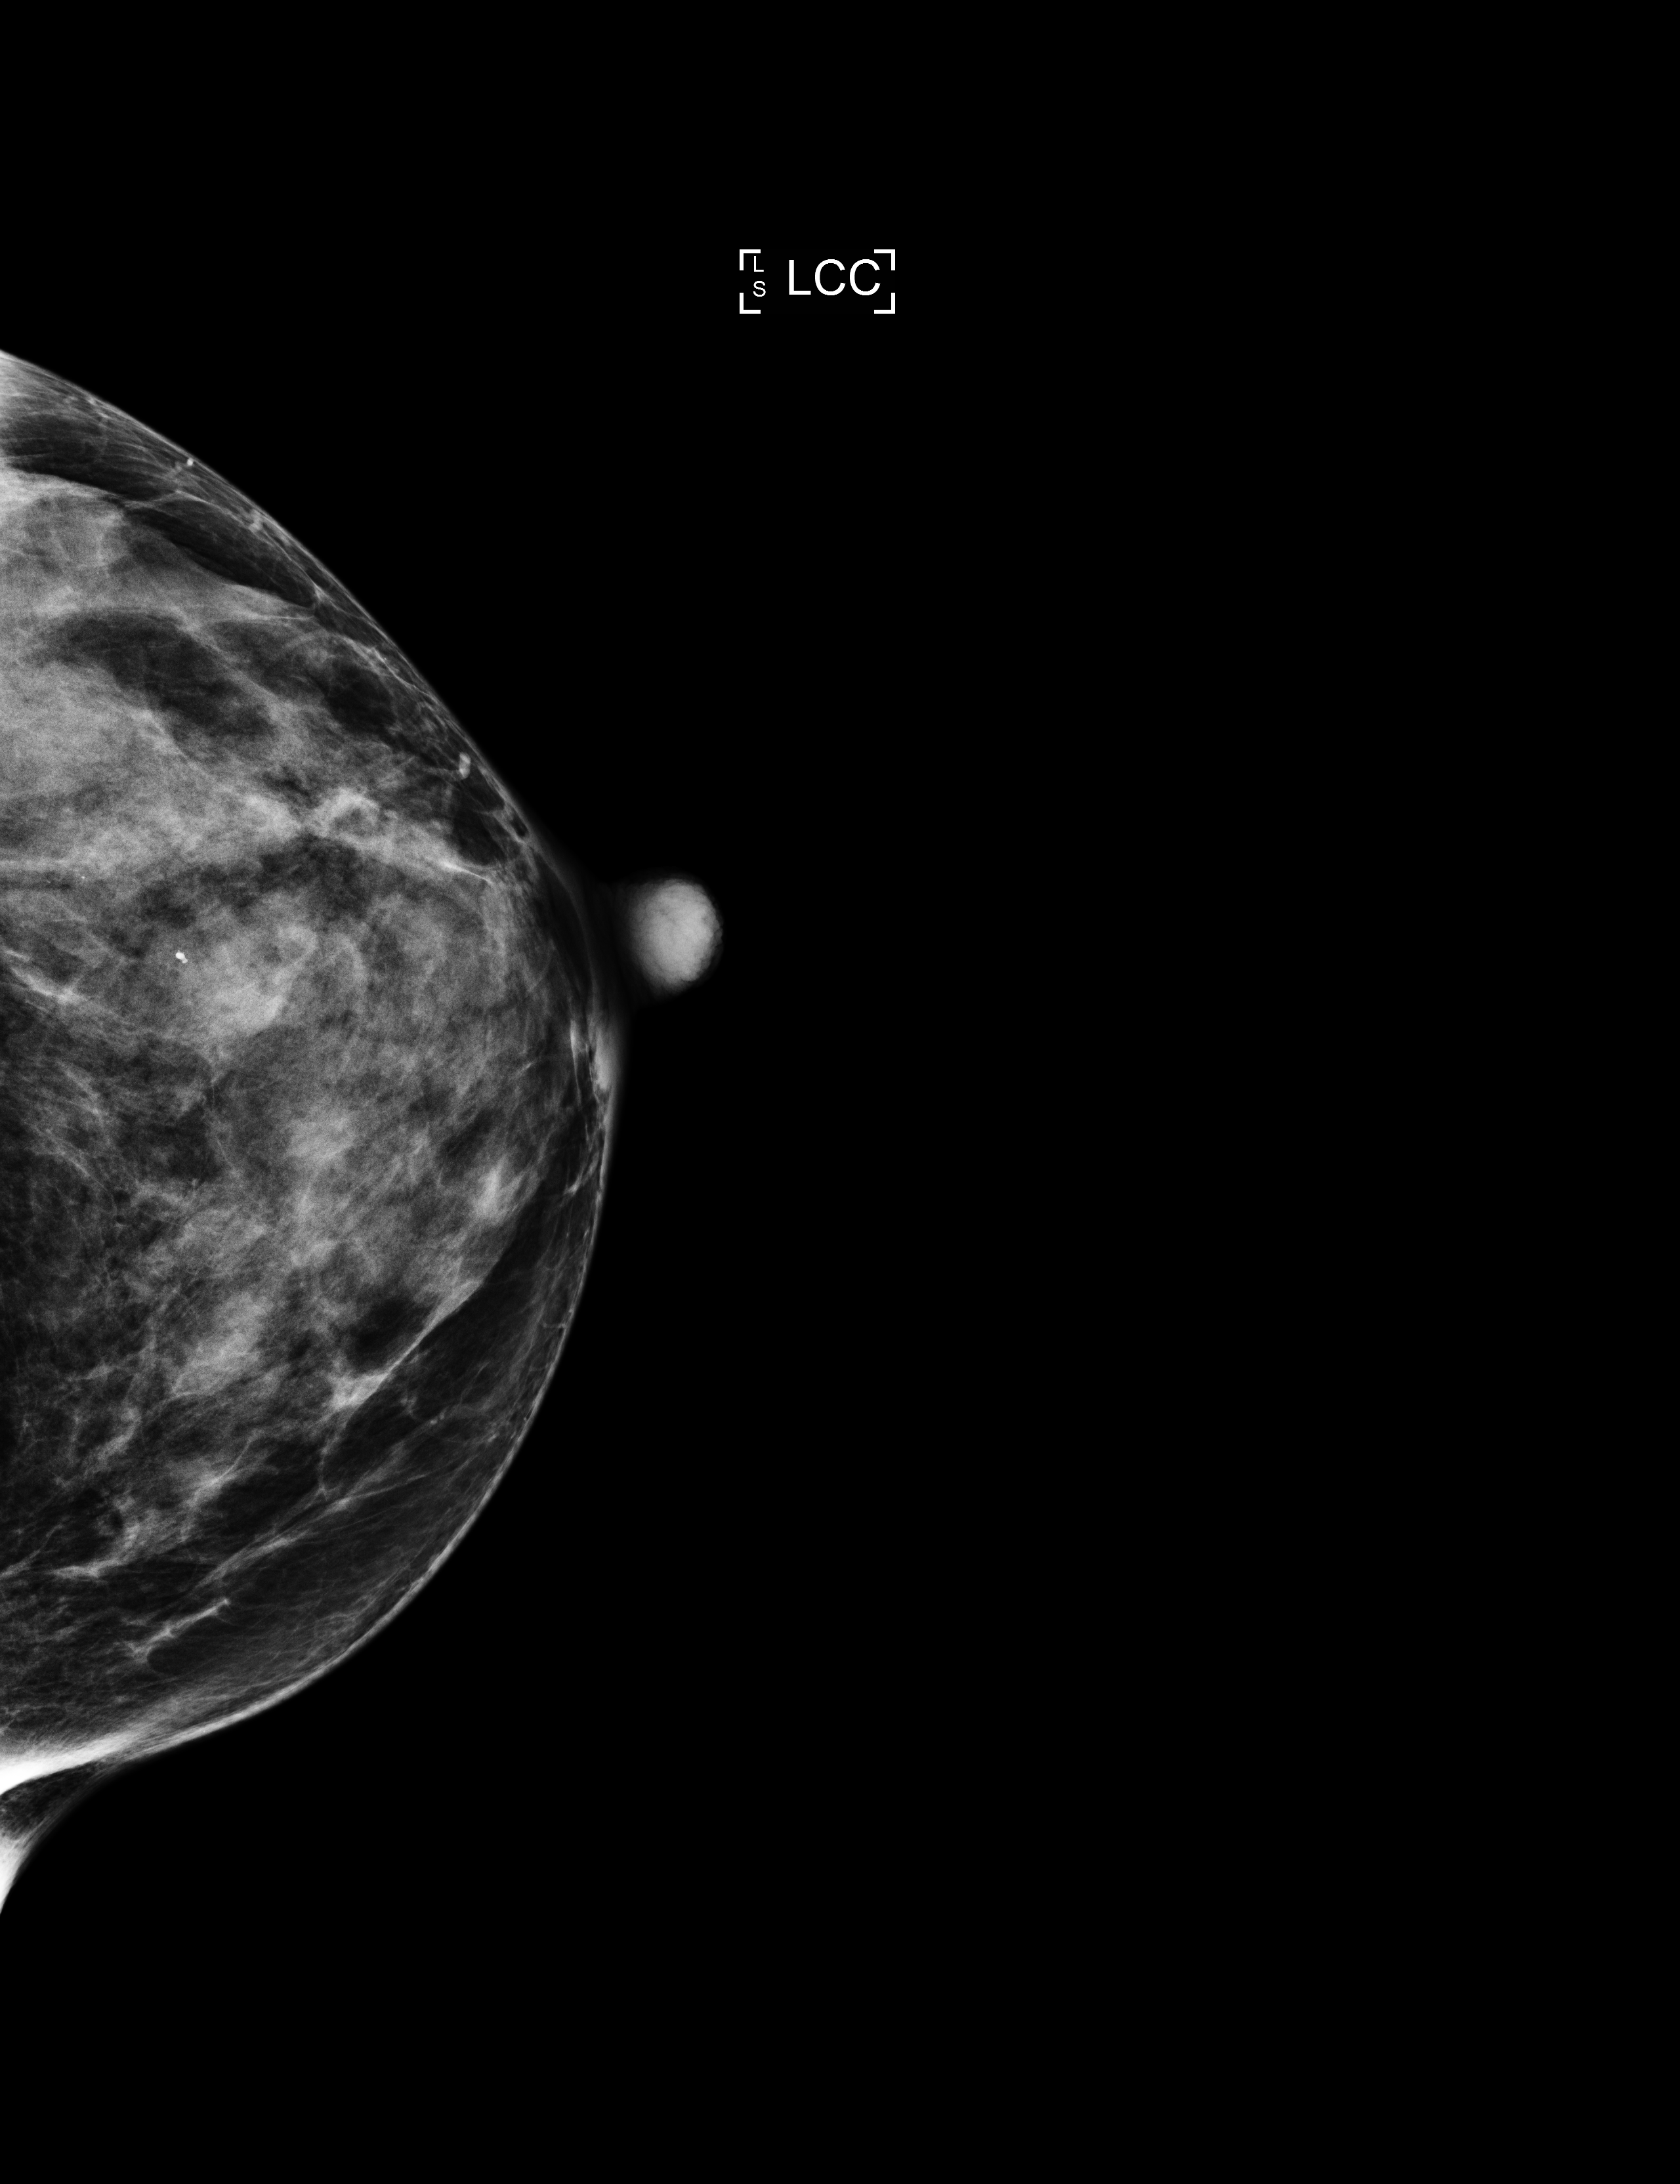
Digital mammogram (FFDM); left breast; cranio-caudal projection; screening examination; system: Selenia Dimensions. Patient: female, 67 years.
Breast density at the screening exam (both breasts): extremely dense (BI-RADS density category d).